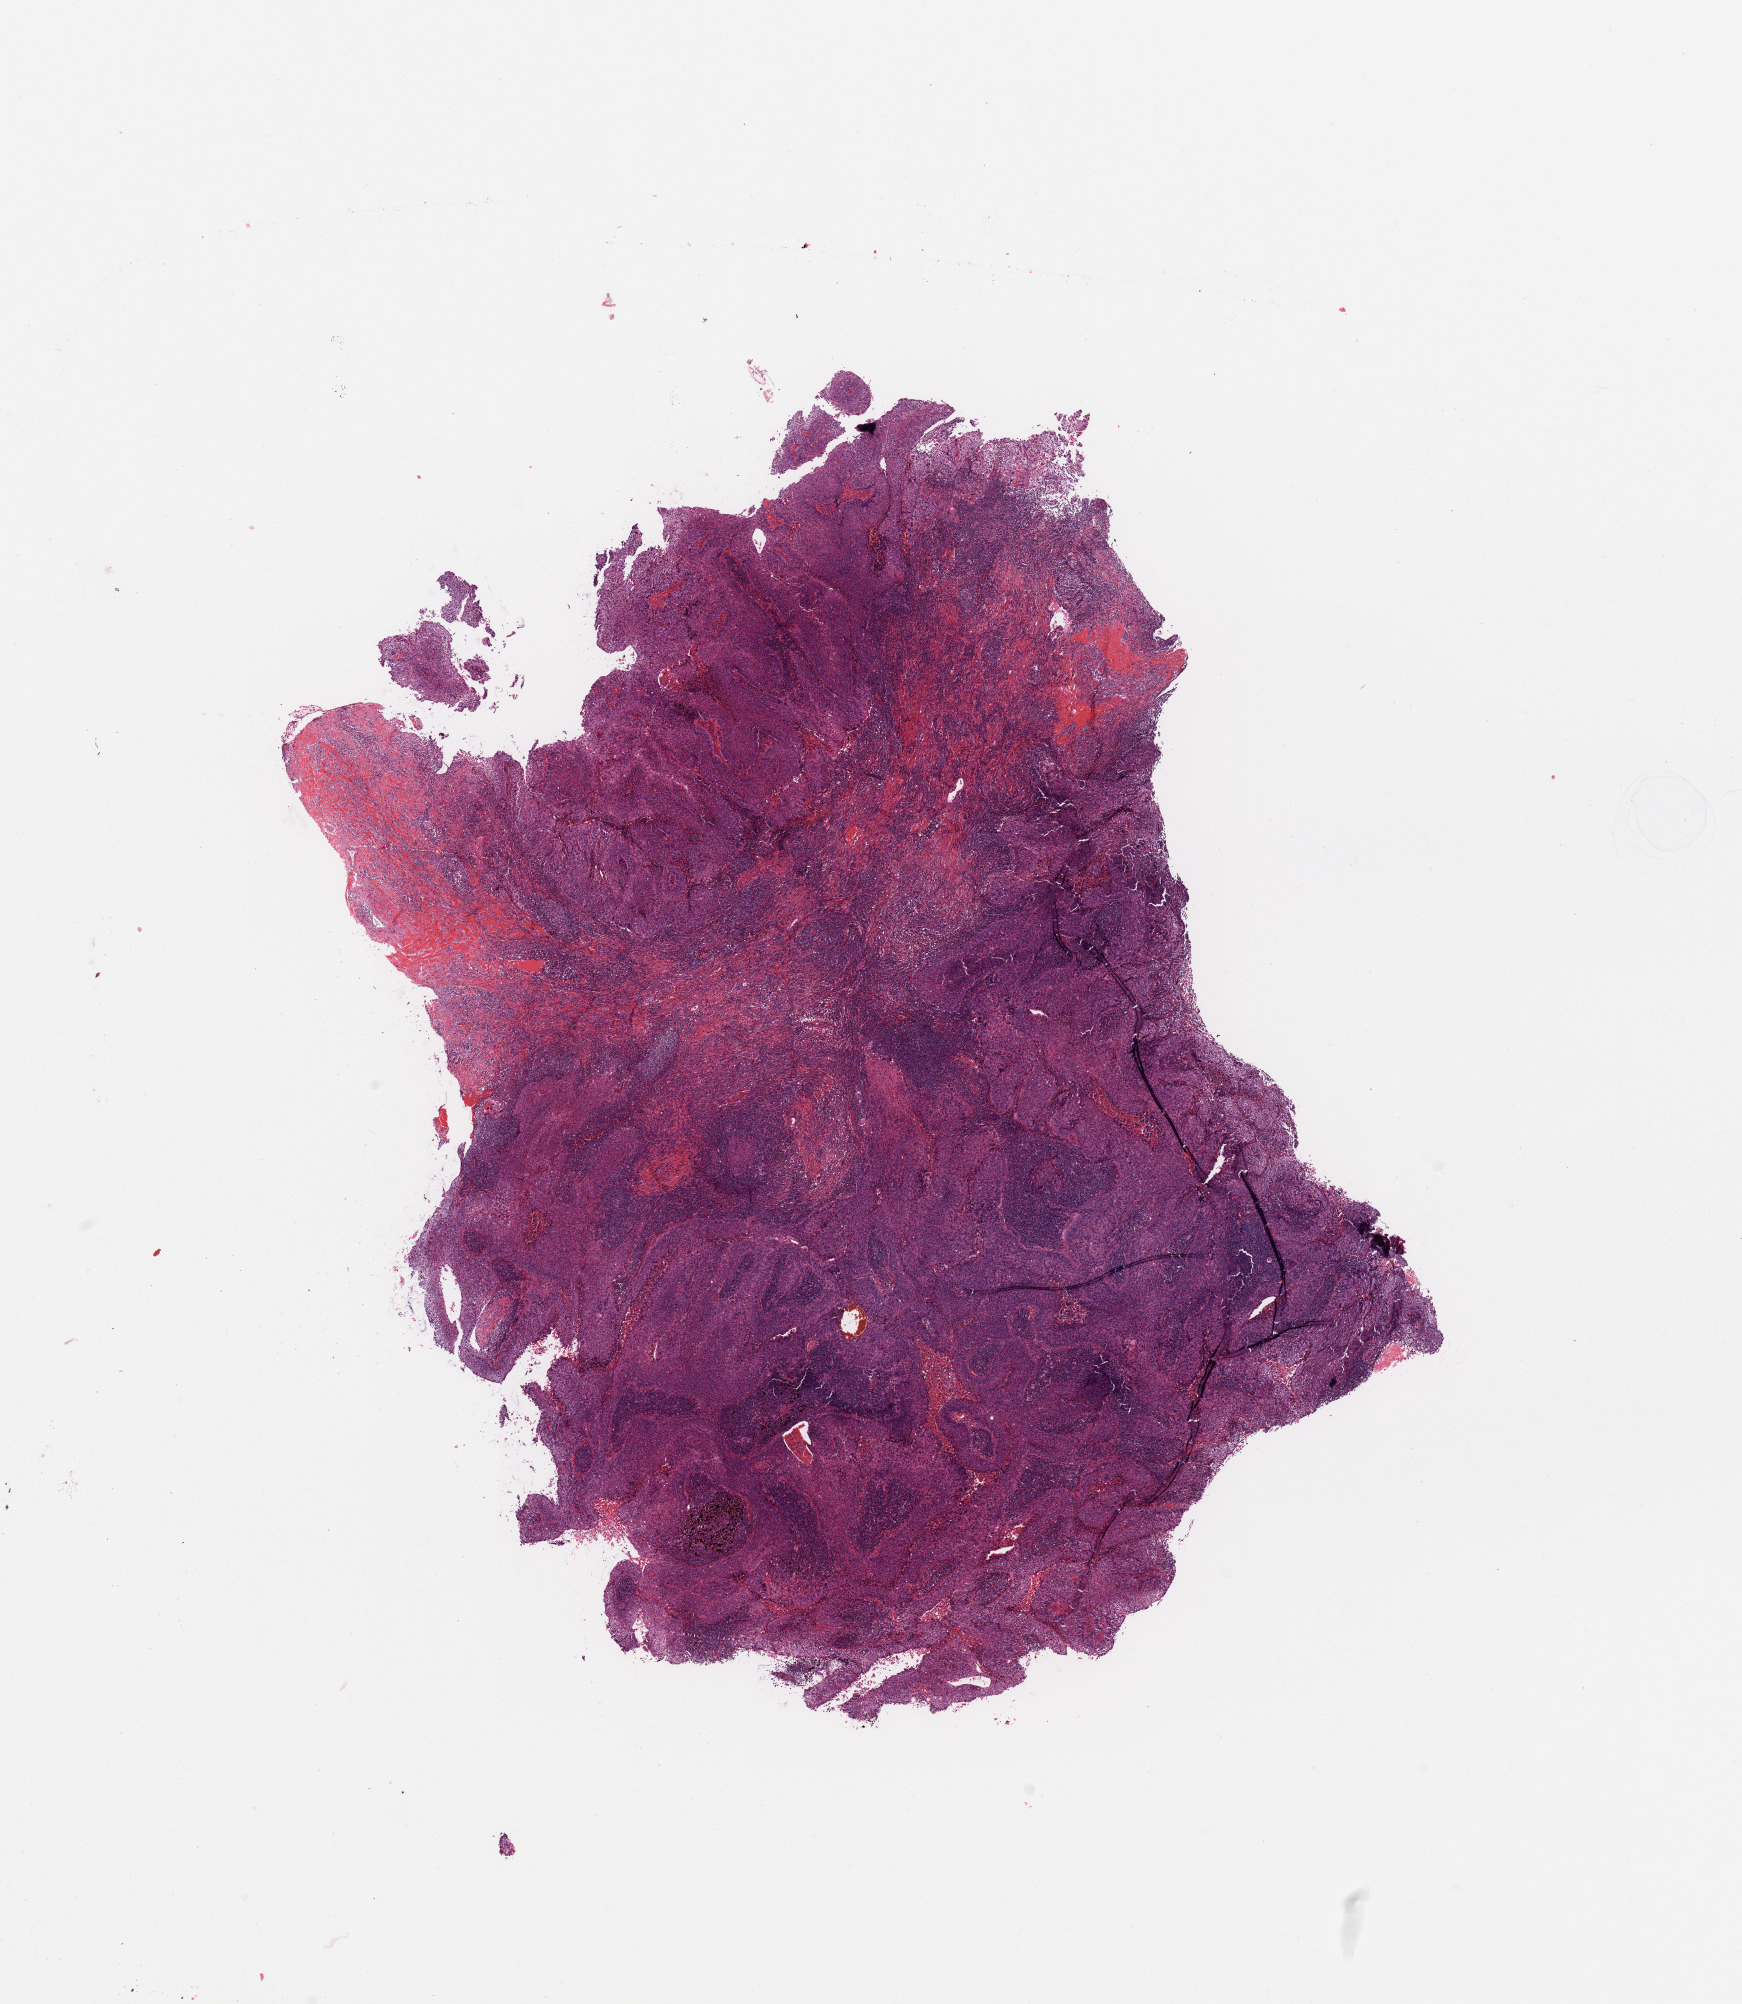
Whole-slide histology image, H&E — shown as a low-resolution overview of the whole scanned area (about 13.8 x 15.9 mm, slide scanned at 20x). Tumour tissue sample, sampled site: lung. Patient: male, age 59 years. Histologic grade: G3 (poorly differentiated). Composition of this section per pathologist review: tumour nuclei 70%, necrosis 5%.
AJCC pathologic stage: IIB. Primary tumour site (as recorded): left upper lobe. Diagnosis: Squamous cell carcinoma, NOS.